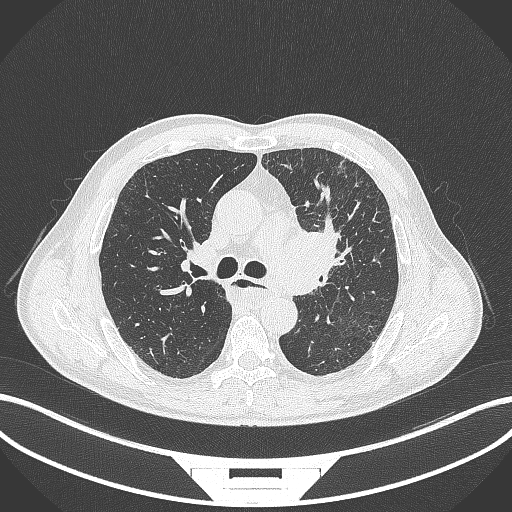
Chest CT, one axial slice. Slice 243 of 411 in the series (ordered by position). Reconstruction kernel B70f. 120 kVp. Lung window (W 1500 / L -600 HU). 1 mm slice thickness. 512 × 512 image matrix. Male patient, age 57 years. From the clinical record (not read from this slice): clinical TNM (as recorded): T2a N1 M0.
Annotated regions visible in this slice (bounding box drawn by a radiologist):
- lung tumour (recorded histology: squamous cell carcinoma): box from (x=272, y=220) to (x=351, y=305) px